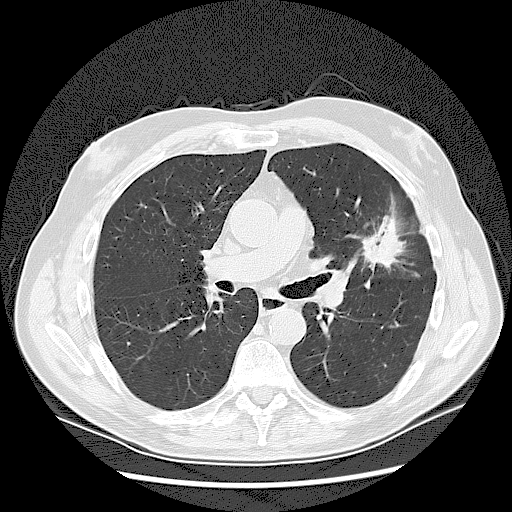
Low-dose screening chest CT, one axial slice; slice 75 of 132 in the series (ordered by position); lung window (W 1500 / L -600 HU); 2.5 mm slice thickness; 512 × 512 image matrix, field of view 380 × 380 mm.
Annotated regions visible in this slice (expert manual segmentation):
- lesion 1 (tumor, upper lobe of left lung): bounding box <362,227,402,265> (left, top, right, bottom; pixels)